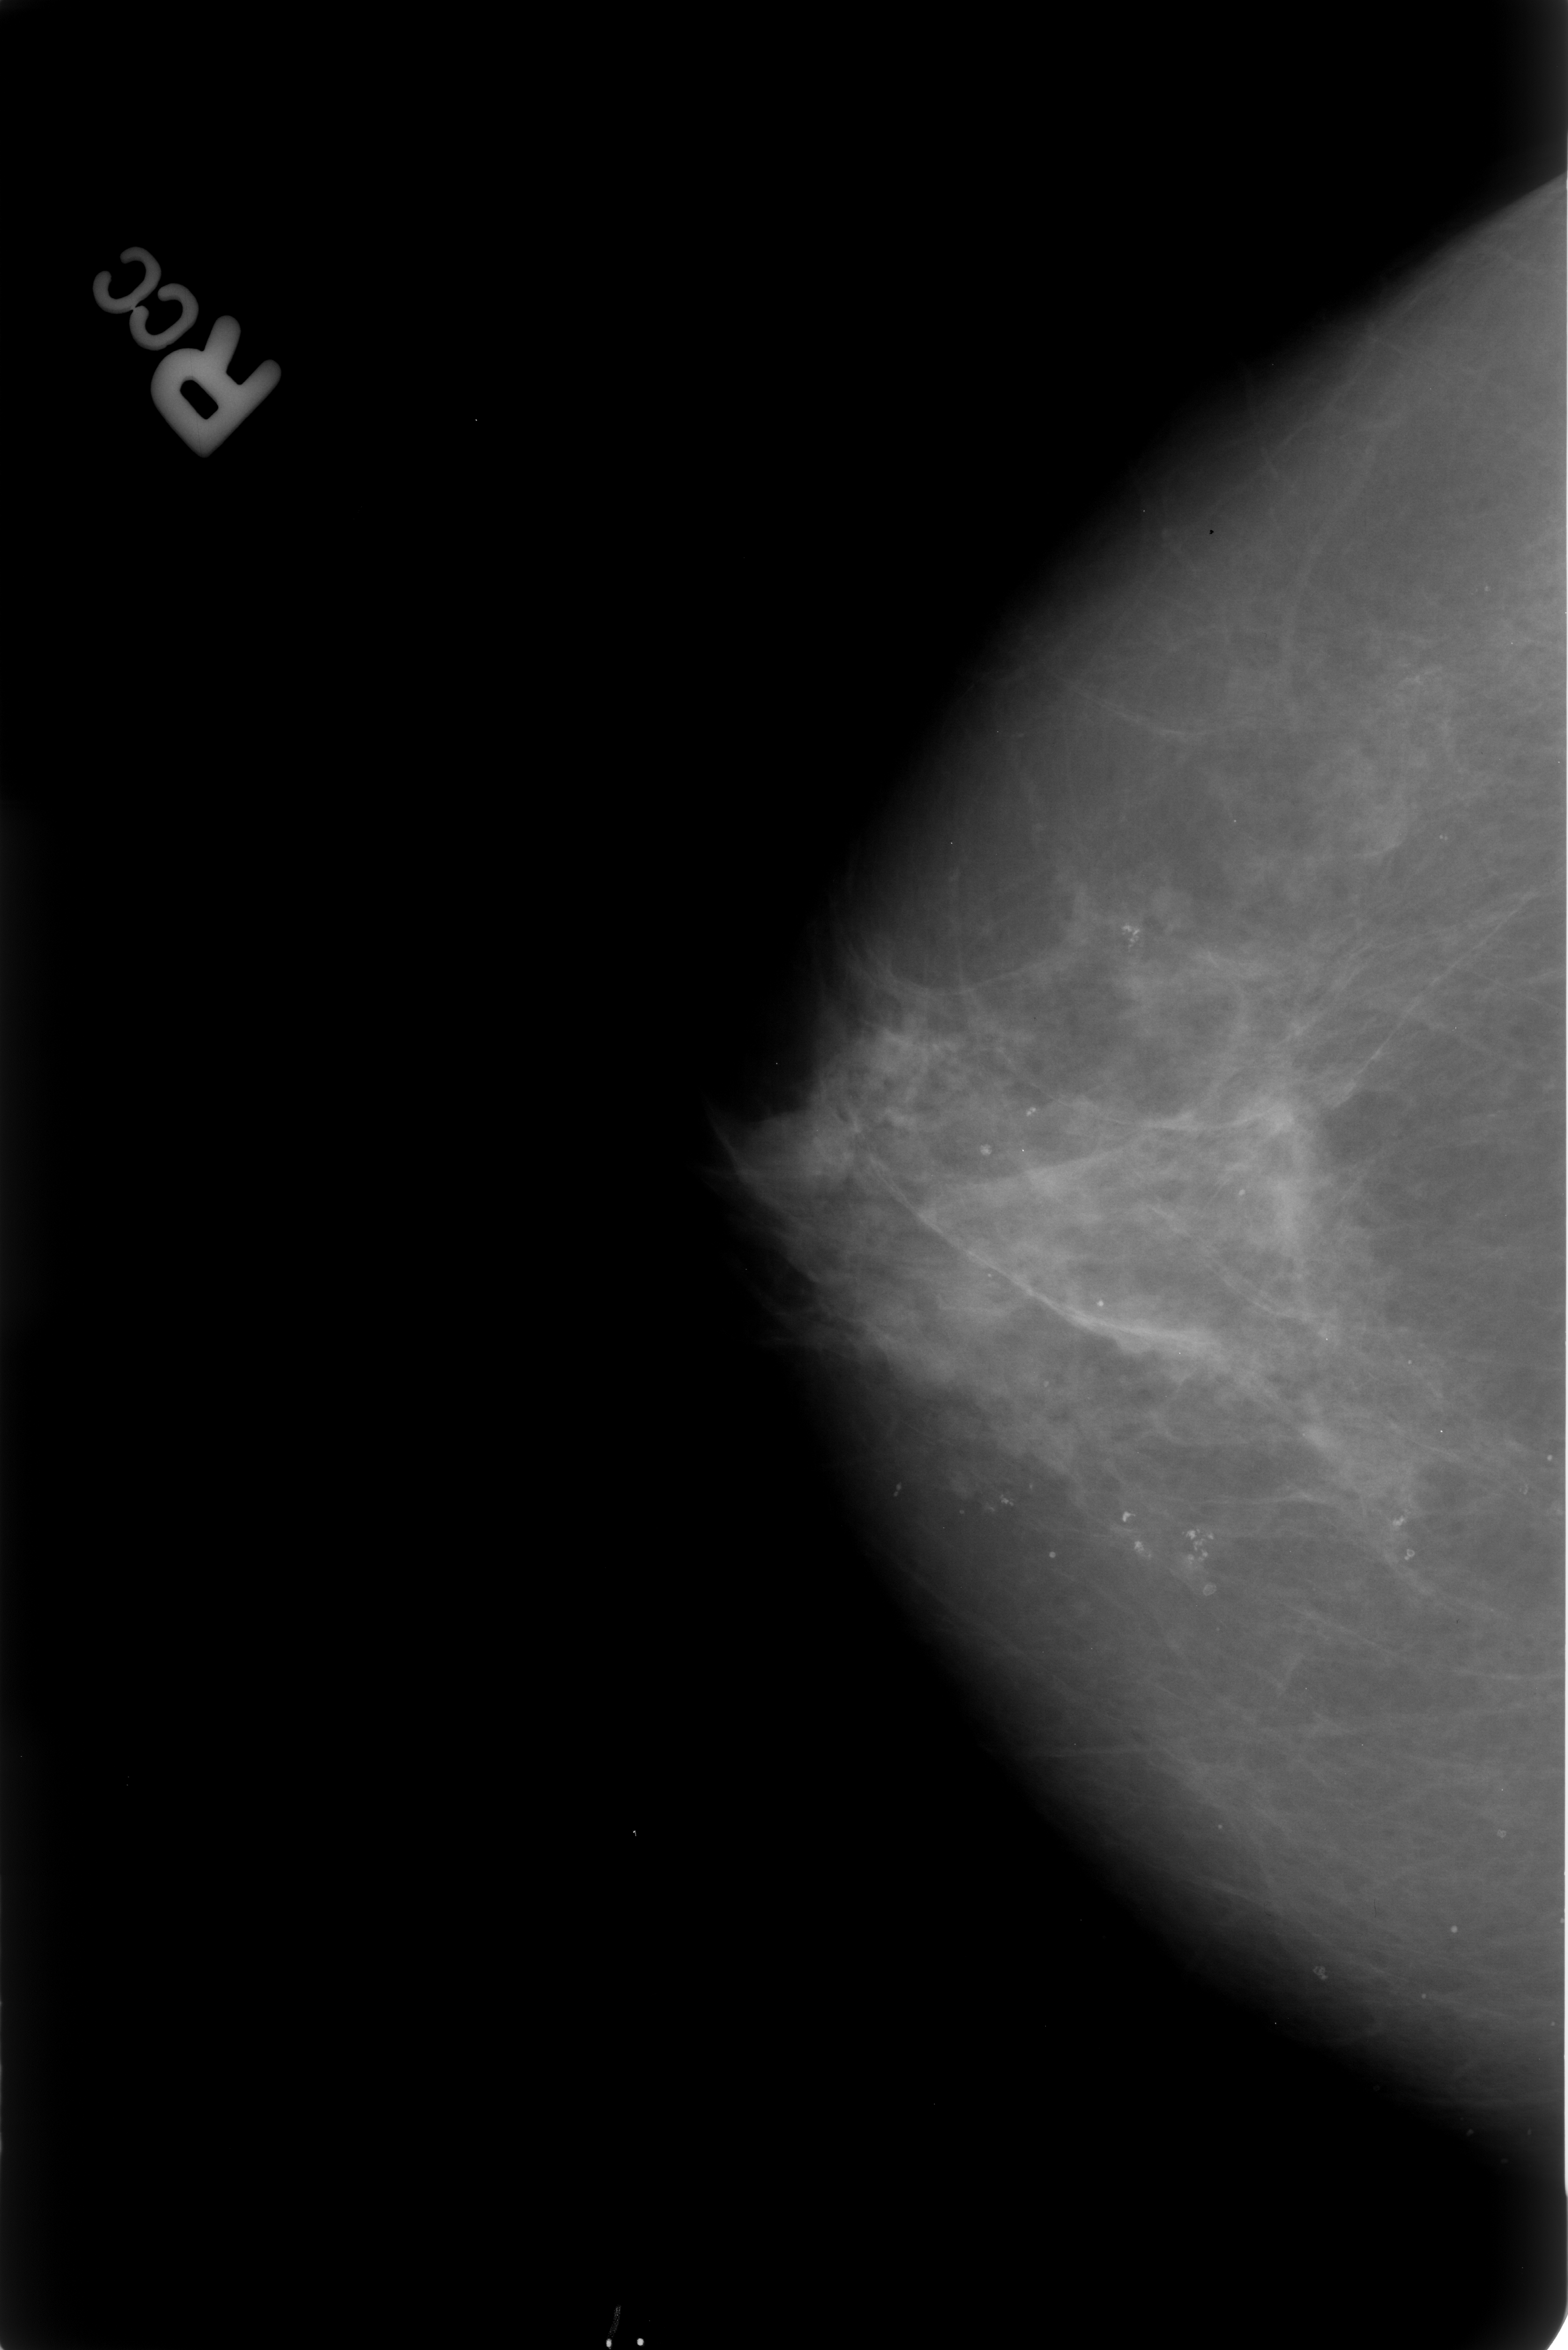
Scanned film-screen mammogram; right breast; CC view; breast composition: scattered fibroglandular densities (BI-RADS density category 2 of 4); 1568 × 2350 image matrix.
Expert-marked regions of interest on this image (one box per marked abnormality):
- Finding 1 of 4: calcifications, morphology pleomorphic, distribution clustered; BI-RADS assessment category 2; subtlety rating 4 on a 1 (subtle) to 5 (obvious) scale; outcome (as recorded, no biopsy): benign without callback (not worked up further): bounding box <963,1075,1081,1193> (left, top, right, bottom; pixels)
- Finding 2 of 4: calcifications, morphology pleomorphic, distribution clustered; BI-RADS assessment category 2; outcome (as recorded, no biopsy): benign without callback (not worked up further): <1096,851,1217,969>
- Finding 3 of 4: calcifications, morphology pleomorphic, distribution clustered; BI-RADS assessment category 2; subtlety rating 4 on a 1 (subtle) to 5 (obvious) scale; outcome (as recorded, no biopsy): benign without callback (not worked up further): <1096,1481,1250,1606>
- Finding 4 of 4: calcifications, morphology pleomorphic, distribution clustered; BI-RADS assessment category 2; subtlety rating 4 on a 1 (subtle) to 5 (obvious) scale; outcome (as recorded, no biopsy): benign without callback (not worked up further): <1361,1485,1449,1590>